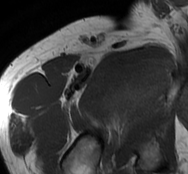
MRI of an extremity soft-tissue mass, one axial slice. Slice 69 of 93 in the series (ordered by position). MR volume resampled by the dataset authors to the PET/CT grid (not the native acquisition matrix). 3.27 mm slice thickness. 188 × 174 image matrix, field of view 184 × 170 mm. Male patient. Case-level facts recorded for this patient, not image findings: histological type: undifferentiated - pleiomorphic; grade: high; site of the primary tumour: right thigh.
Structures marked on this image (expert contour drawn on MRI and transferred to this co-registered scan by the dataset authors):
- gross tumour volume including surrounding oedema: box from (x=104, y=49) to (x=176, y=123) px
- gross tumour volume (mass): (x=104, y=53)–(x=172, y=120)